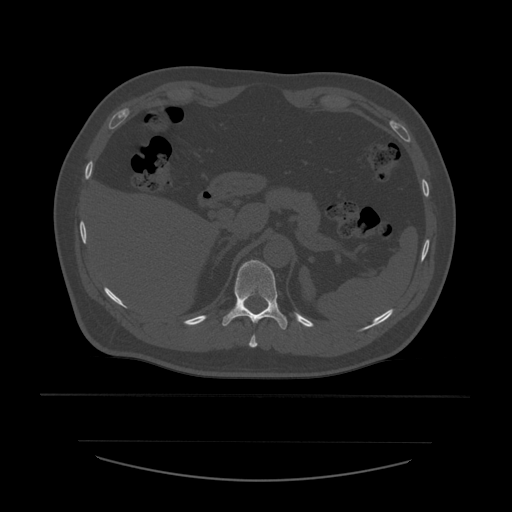
CT including the spine, one axial slice; slice 276 of 532 in the series (ordered by position); reconstruction kernel STANDARD; 120 kVp; bone window (W 1800 / L 400 HU); 512 × 512 image matrix, field of view 441 × 441 mm. Patient age 44 years. Case-level facts recorded for this patient, not image findings: primary cancer: soft tissue sarcoma.
Outlined on this slice (semi-automatic segmentation, software-assisted and operator-edited):
- T10 vertebra: bounding box <249,334,258,348> (left, top, right, bottom; pixels)
- T11 vertebra: <222,260,288,330>